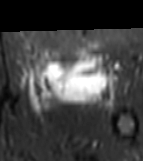
MRI of an extremity soft-tissue mass, one axial slice. Position 39 of 81 along the scan axis. STIR. MR volume resampled by the dataset authors to the PET/CT grid (not the native acquisition matrix). 143 × 161 image matrix, field of view 140 × 157 mm. Female patient. Case-level facts recorded for this patient, not image findings: histological type: myxofibrosarcoma; grade: intermediate; site of the primary tumour: left thigh.
Outlined on this slice (expert contour drawn on MRI and transferred to this co-registered scan by the dataset authors):
- gross tumour volume including surrounding oedema: bounding box (x1, y1, x2, y2) in pixels: (26, 51, 118, 111)
- gross tumour volume (mass): (33, 51, 105, 100)